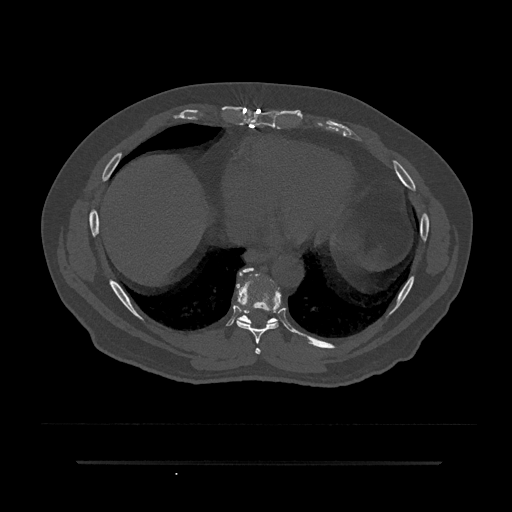
CT including the spine, one axial slice; slice 410 of 797 in the series (ordered by position); reconstruction kernel Br40s/3; 120 kVp; bone window (W 1800 / L 400 HU); 0.5 mm slice thickness; 512 × 512 image matrix, field of view 464 × 464 mm. Male patient, age 59 years. From the clinical record (not read from this slice): primary cancer: bile ducts.
Outlined on this slice (semi-automatically segmented with operator editing):
- T7 vertebra: box from (x=255, y=348) to (x=261, y=354) px
- T8 vertebra: (x=236, y=268)–(x=282, y=353)
- T9 vertebra: (x=236, y=268)–(x=277, y=325)